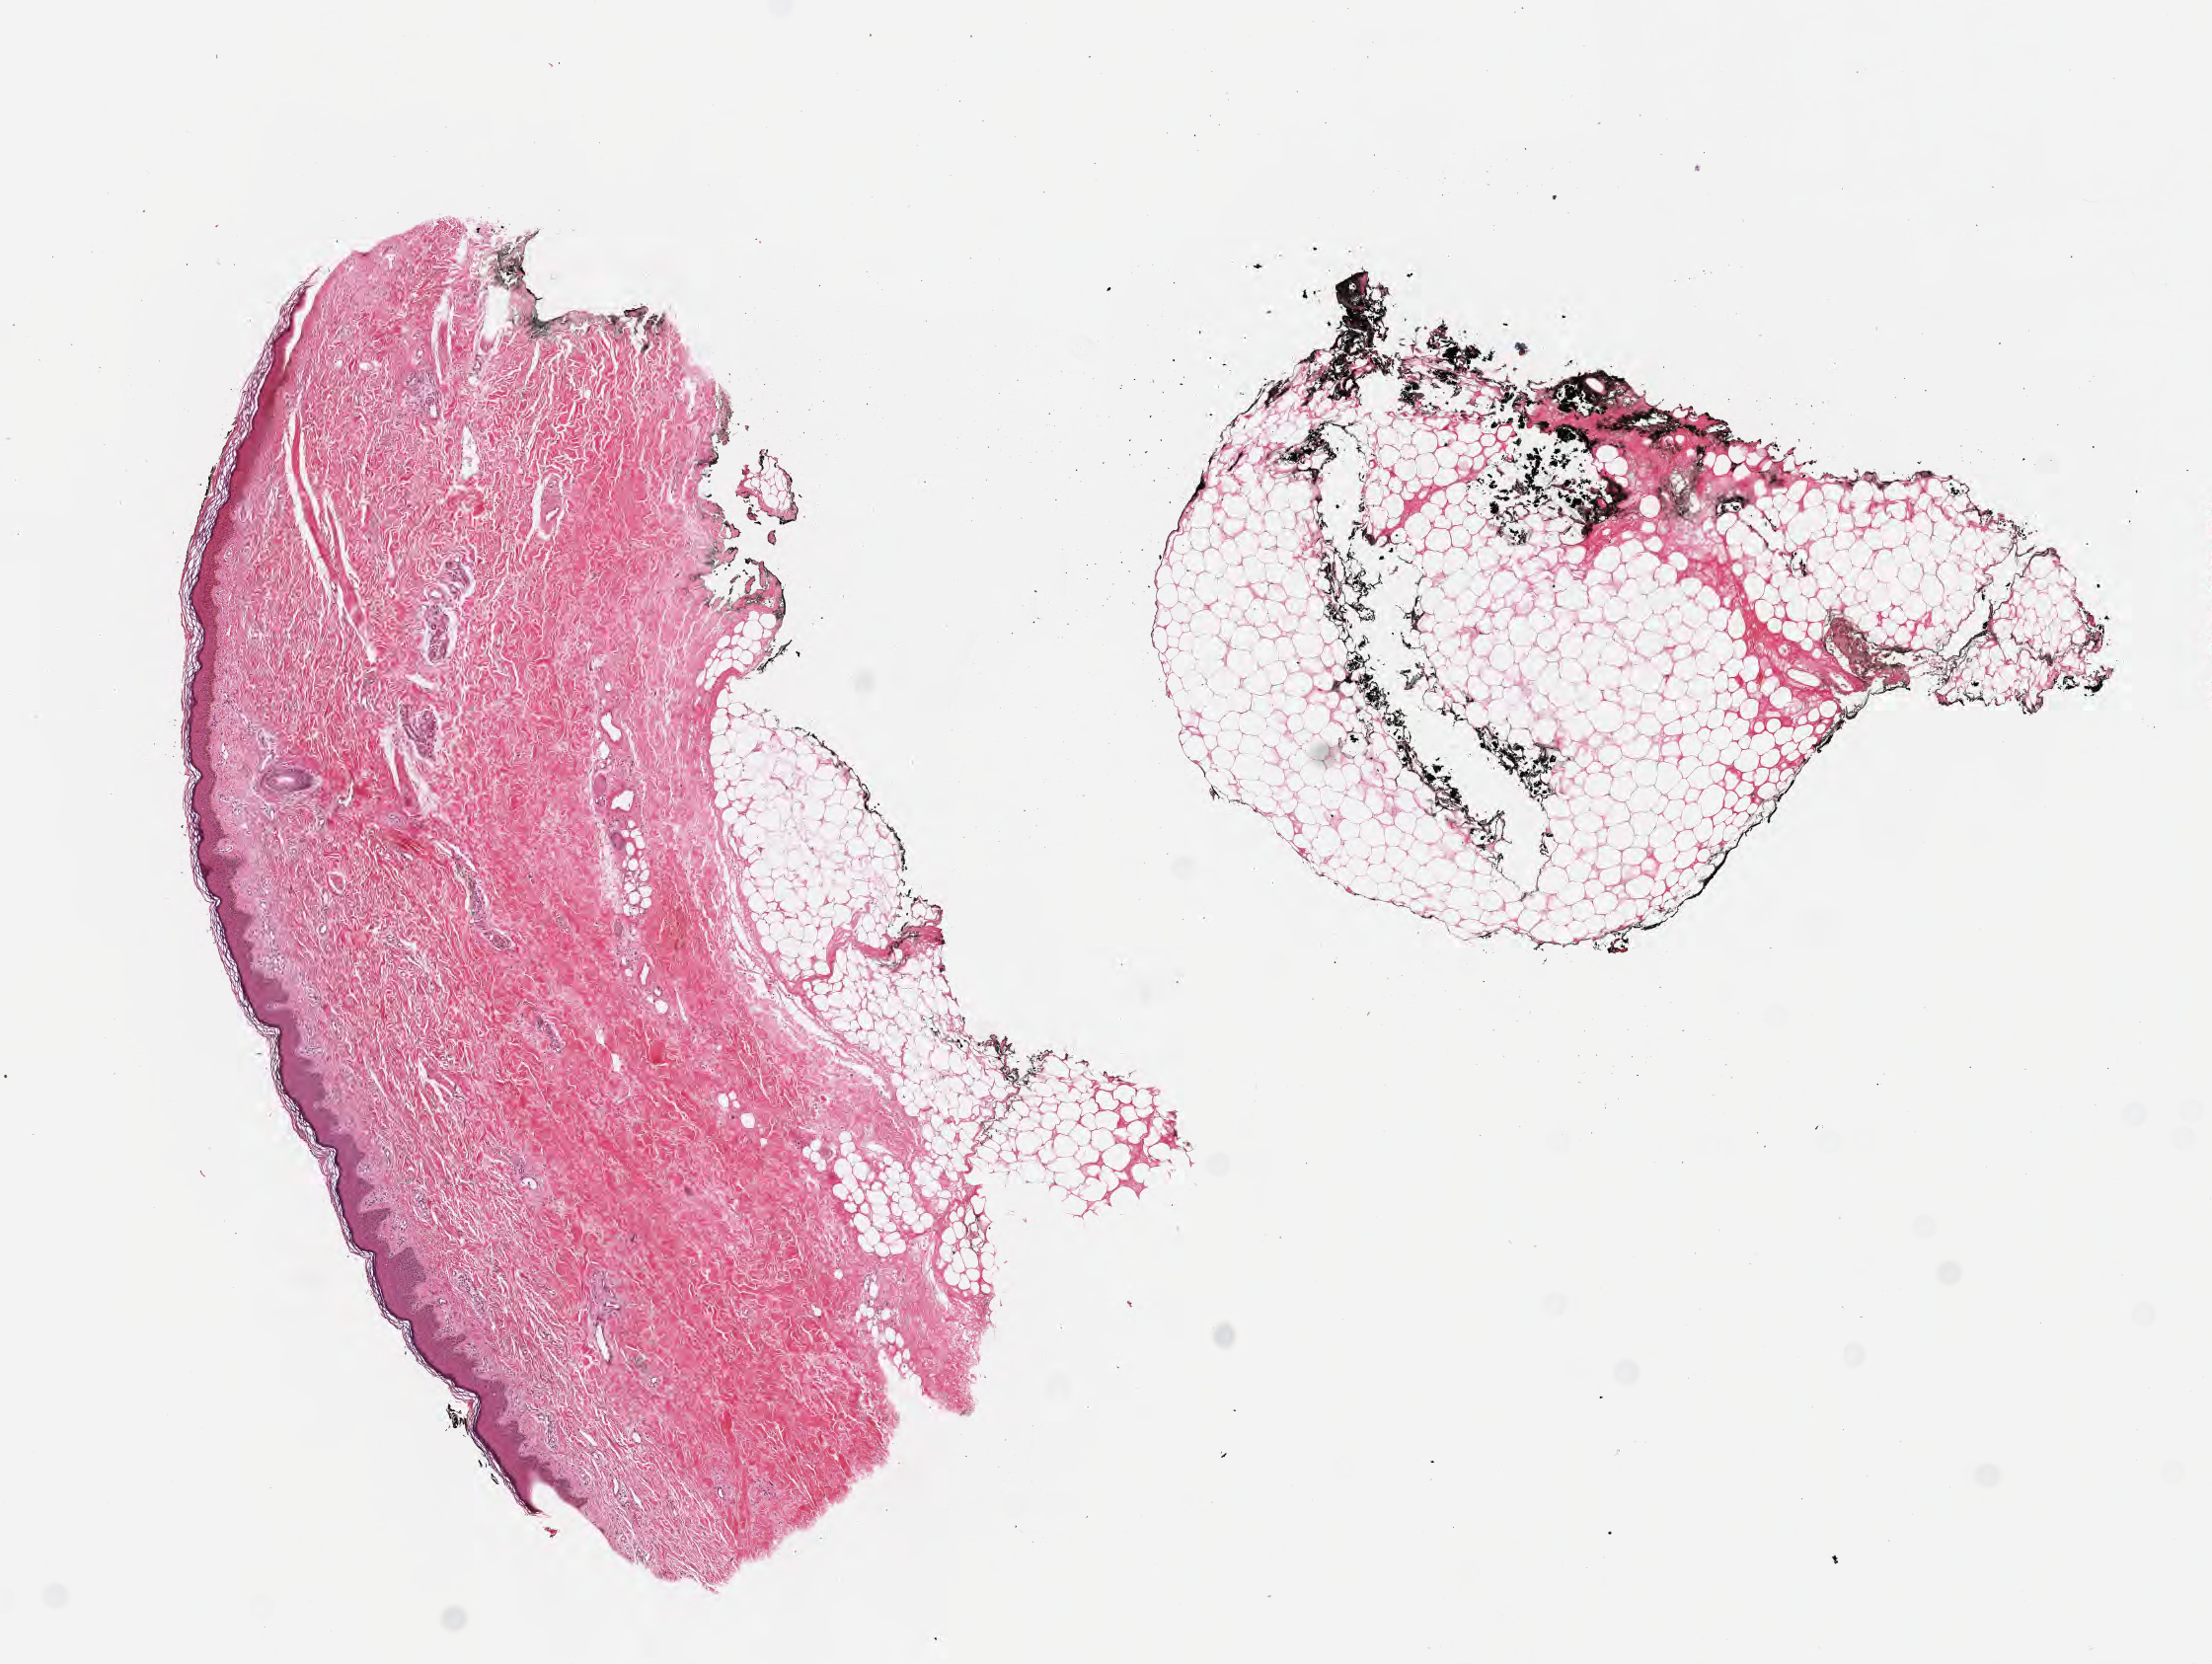
Digitized haematoxylin and eosin-stained section — whole scanned area (about 9.1 x 6.8 mm) shown as a low-resolution overview. Formalin-fixed, paraffin-embedded (FFPE) tissue. Specimen: non-tumor (normal tissue) sample from a patient with burkitt lymphoma, NOS. Patient female; aged 16. Pathologist review of this section (percent, as recorded): tumor cells 0%, tumor nuclei 0%, stromal cells 0%, necrosis 0%, normal cells 100%. Inflammatory infiltration, as recorded: lymphocyte infiltration 80%, monocyte infiltration 5%, neutrophil infiltration 0%.
This section: non-tumor tissue sample; the patient's diagnosis is given above.